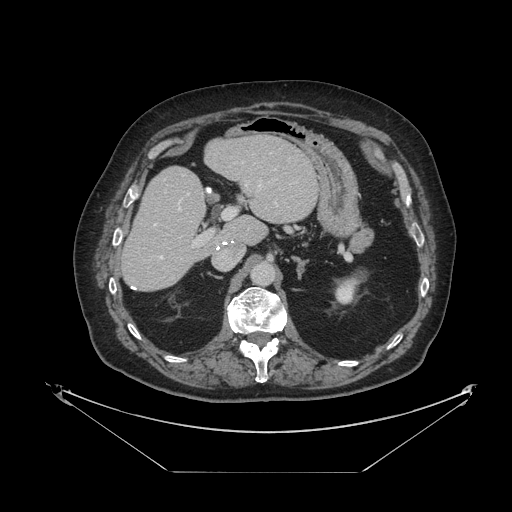
Contrast-enhanced abdominal CT, one axial slice. Slice 60 of 121 in the series (ordered by position). Reconstruction kernel STANDARD. Soft-tissue window (W 400 / L 40 HU). 2.5 mm slice thickness. 512 × 512 image matrix, field of view 500 × 500 mm. Male patient, age 68 years. Case-level facts recorded for this patient, not image findings: diagnosis: colorectal cancer liver metastases, imaged before liver resection; multiple liver metastases: no; largest metastasis: 4 cm; chemotherapy before resection: yes.
Annotated regions visible in this slice (outlined manually by an expert reader):
- hepatic veins: bounding box (x1, y1, x2, y2) in pixels: (160, 169, 278, 259)
- liver: (122, 136, 318, 291)
- planned liver remnant (the part of the liver to remain after resection): (122, 136, 318, 291)
- portal vein (with intrahepatic branches): (191, 181, 262, 248)